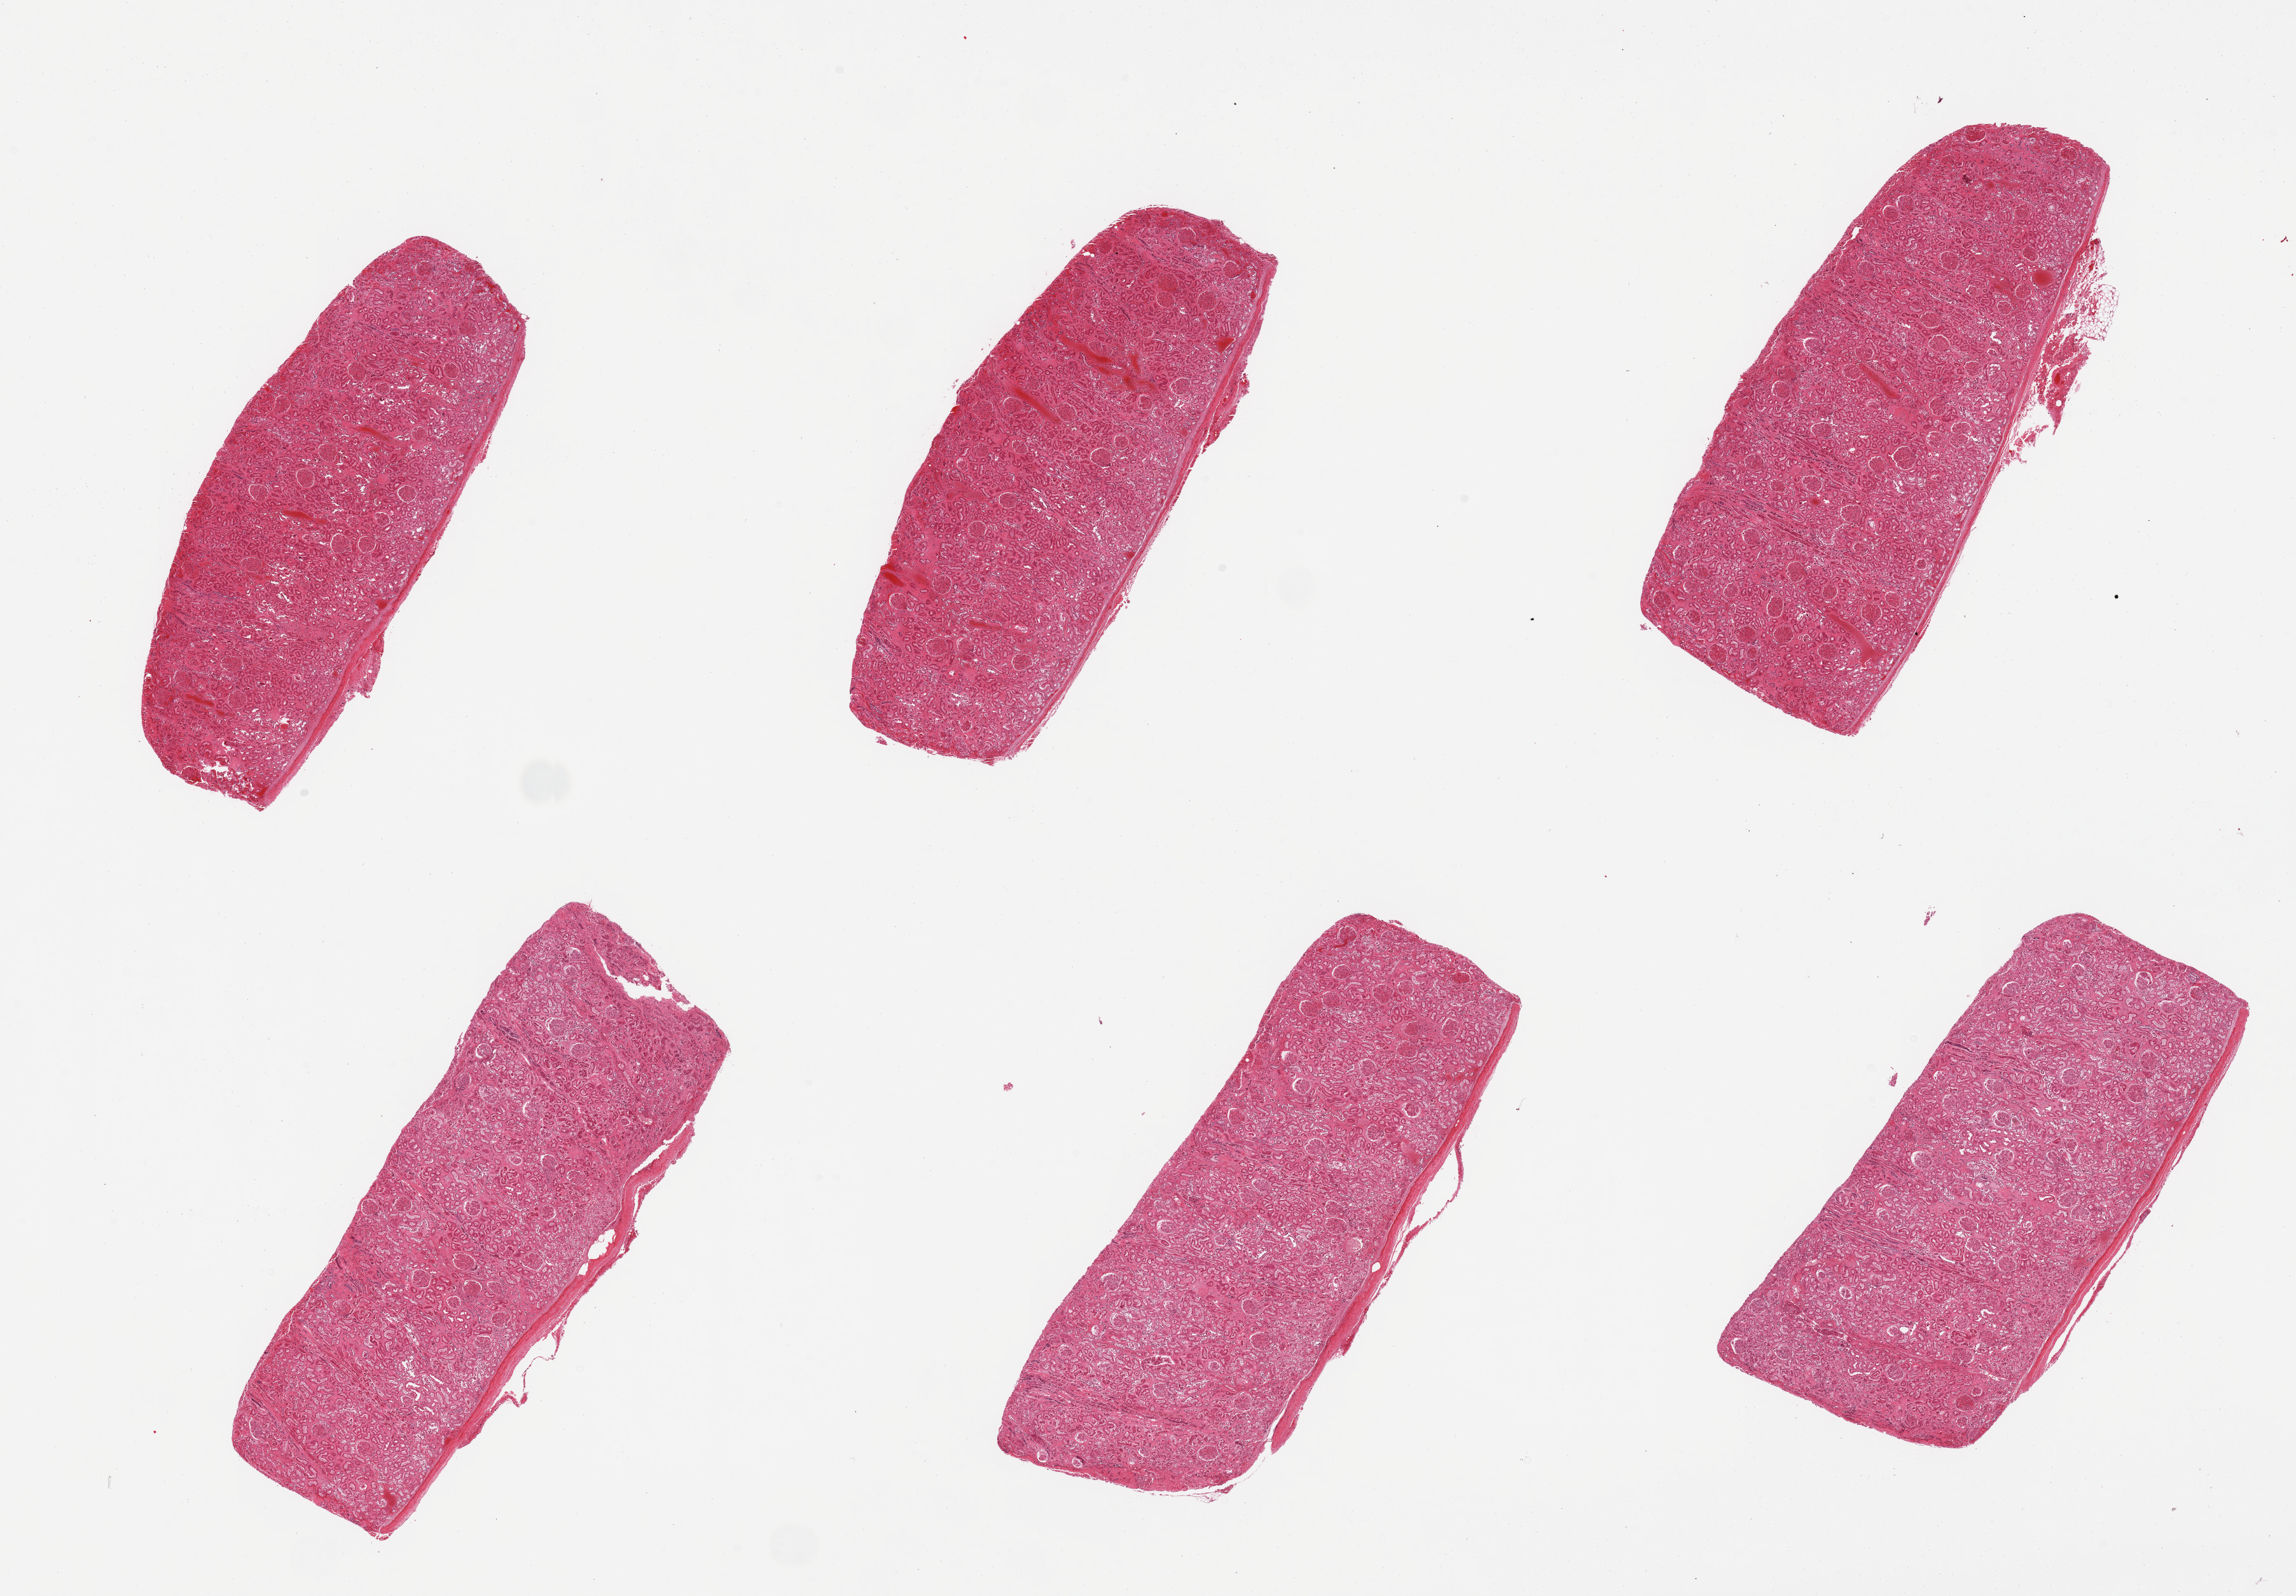
Whole-slide image, hematoxylin and eosin (H&E) stain, brightfield — a low-resolution overview of the entire scanned area, about 28.5 x 19.8 mm (slide scanned at 20x), PAXgene-fixed, paraffin-embedded tissue, section of renal cortex (target tissue), donor tissue sample. Male donor.
- pathologist's review note for this sample: 6 pieces. Congested